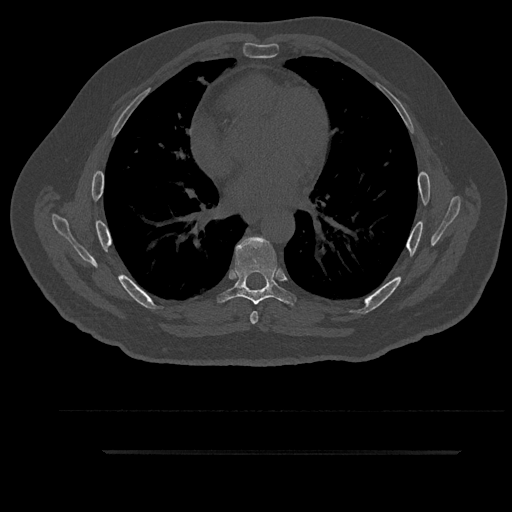
CT including the spine, one axial slice. Position 537 of 797 along the scan axis. Reconstruction kernel Br40s/3. Bone window (W 1800 / L 400 HU). 512 × 512 image matrix. Patient: male, 63 years. From the clinical record (not read from this slice): primary cancer: renal; vertebrae with lytic lesions (as recorded): T8.
Structures marked on this image (semi-automatically segmented with operator editing):
- T6 vertebra: bounding box (x1, y1, x2, y2) in pixels: (250, 237, 259, 324)
- T7 vertebra: (216, 236, 296, 306)